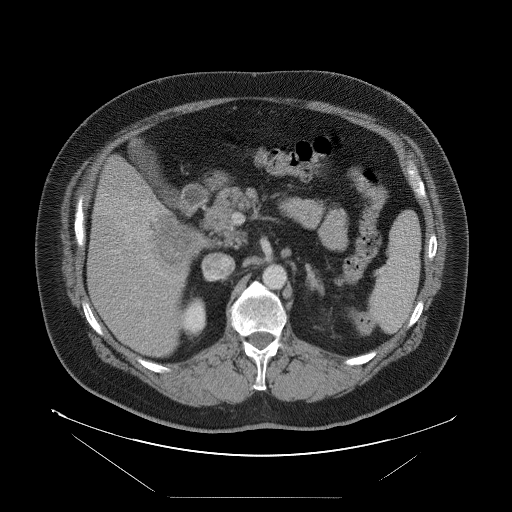
Contrast-enhanced abdominal CT, one axial slice; slice 47 of 114 in the series (ordered by position); 120 kVp; intravenous contrast given; soft-tissue window (W 400 / L 40 HU); 5 mm slice thickness; 512 × 512 image matrix, field of view 500 × 500 mm. Male patient, age 61 years. From the clinical record (not read from this slice): diagnosis: colorectal cancer liver metastases, imaged before liver resection; multiple liver metastases: no; largest metastasis: 6.5 cm; disease in both lobes: yes.
Outlined on this slice (manually delineated by an expert):
- liver: box from (x=88, y=157) to (x=209, y=357) px
- liver metastasis: (x=157, y=215)–(x=205, y=270)